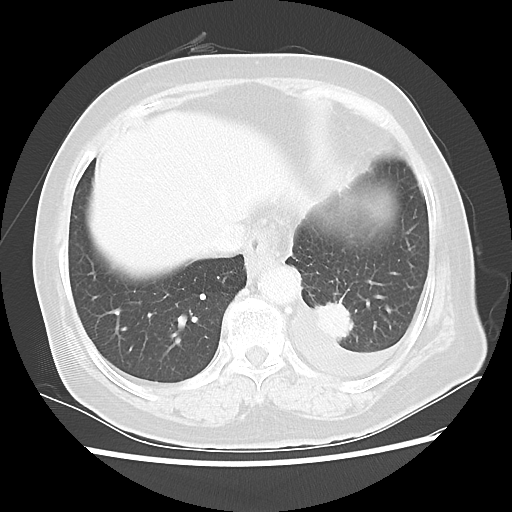
Chest CT, one axial slice; slice 7 of 40 in the series (ordered by position); 100 kVp; lung window (W 1500 / L -600 HU); 512 × 512 image matrix, field of view 343 × 343 mm. Female patient, age 68 years. Case-level facts recorded for this patient, not image findings: clinical TNM (as recorded): T1c N0 M1.
Annotated regions visible in this slice (bounding box drawn by a radiologist):
- lung tumour (recorded histology: adenocarcinoma): bounding box [x1, y1, x2, y2] px = [315, 300, 359, 344]